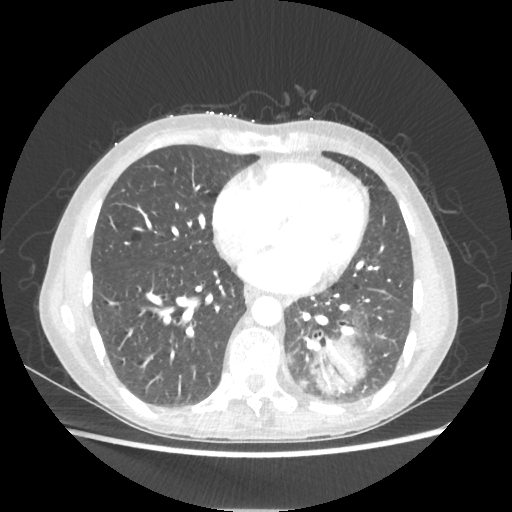
Chest CT, one axial slice; slice 83 of 221 in the series (ordered by position); reconstruction kernel STANDARD; 80 kVp; lung window (W 1500 / L -600 HU); 1.25 mm slice thickness; 512 × 512 image matrix. Female patient, age 53 years. Case-level facts recorded for this patient, not image findings: clinical TNM (as recorded): T3 N0 M0.
Outlined on this slice (rectangle marked by the reading radiologist):
- lung tumour (recorded histology: adenocarcinoma): box from (x=312, y=339) to (x=364, y=395) px